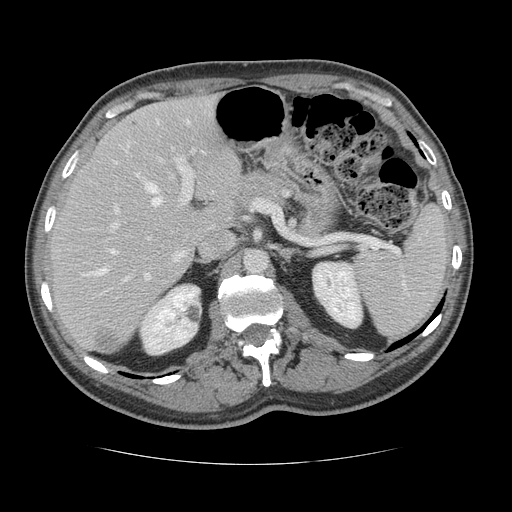
Contrast-enhanced abdominal CT, one axial slice. Position 82 of 134 along the scan axis. Reconstruction kernel STANDARD. 120 kVp. Intravenous contrast given. Soft-tissue window (W 400 / L 40 HU). 2.5 mm slice thickness. 512 × 512 image matrix, field of view 377 × 377 mm. Male patient, age 68 years. From the clinical record (not read from this slice): diagnosis: colorectal cancer liver metastases, imaged before liver resection; multiple liver metastases: yes; largest metastasis: 2.2 cm.
Annotated regions visible in this slice (manually delineated by an expert):
- hepatic veins: bounding box (x1, y1, x2, y2) in pixels: (82, 120, 204, 276)
- liver: (51, 95, 245, 353)
- planned liver remnant (the part of the liver to remain after resection): (51, 95, 244, 338)
- portal vein (with intrahepatic branches): (112, 119, 196, 280)
- liver metastasis: (95, 330, 122, 352)